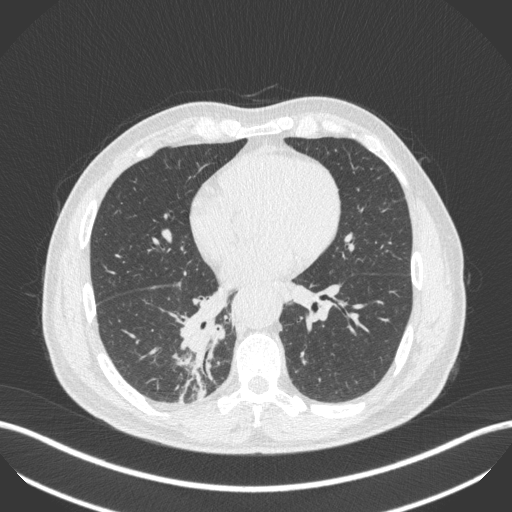
Chest CT, one axial slice; slice 211 of 451 in the series (ordered by position); lung window (W 1500 / L -600 HU); 1 mm slice thickness; 512 × 512 image matrix, field of view 400 × 400 mm. Patient: male, 61 years. Case-level facts recorded for this patient, not image findings: clinical TNM (as recorded): T1 N0 M0.
Annotated regions visible in this slice (bounding box drawn by a radiologist):
- lung tumour (recorded histology: small cell carcinoma): bounding box <174,316,222,399> (left, top, right, bottom; pixels)